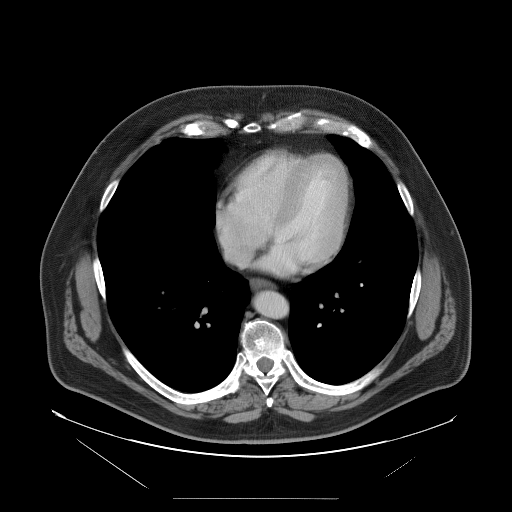
Contrast-enhanced abdominal CT, one axial slice; 120 kVp; intravenous contrast given; soft-tissue window (W 400 / L 40 HU); 5 mm slice thickness; 512 × 512 image matrix, field of view 500 × 500 mm. Male patient, age 61 years. From the clinical record (not read from this slice): diagnosis: colorectal cancer liver metastases, imaged before liver resection; multiple liver metastases: no; largest metastasis: 6.5 cm; chemotherapy before resection: no.
Annotated regions visible in this slice (manually delineated by an expert):
- hepatic veins: bounding box [x1, y1, x2, y2] px = [218, 214, 268, 267]